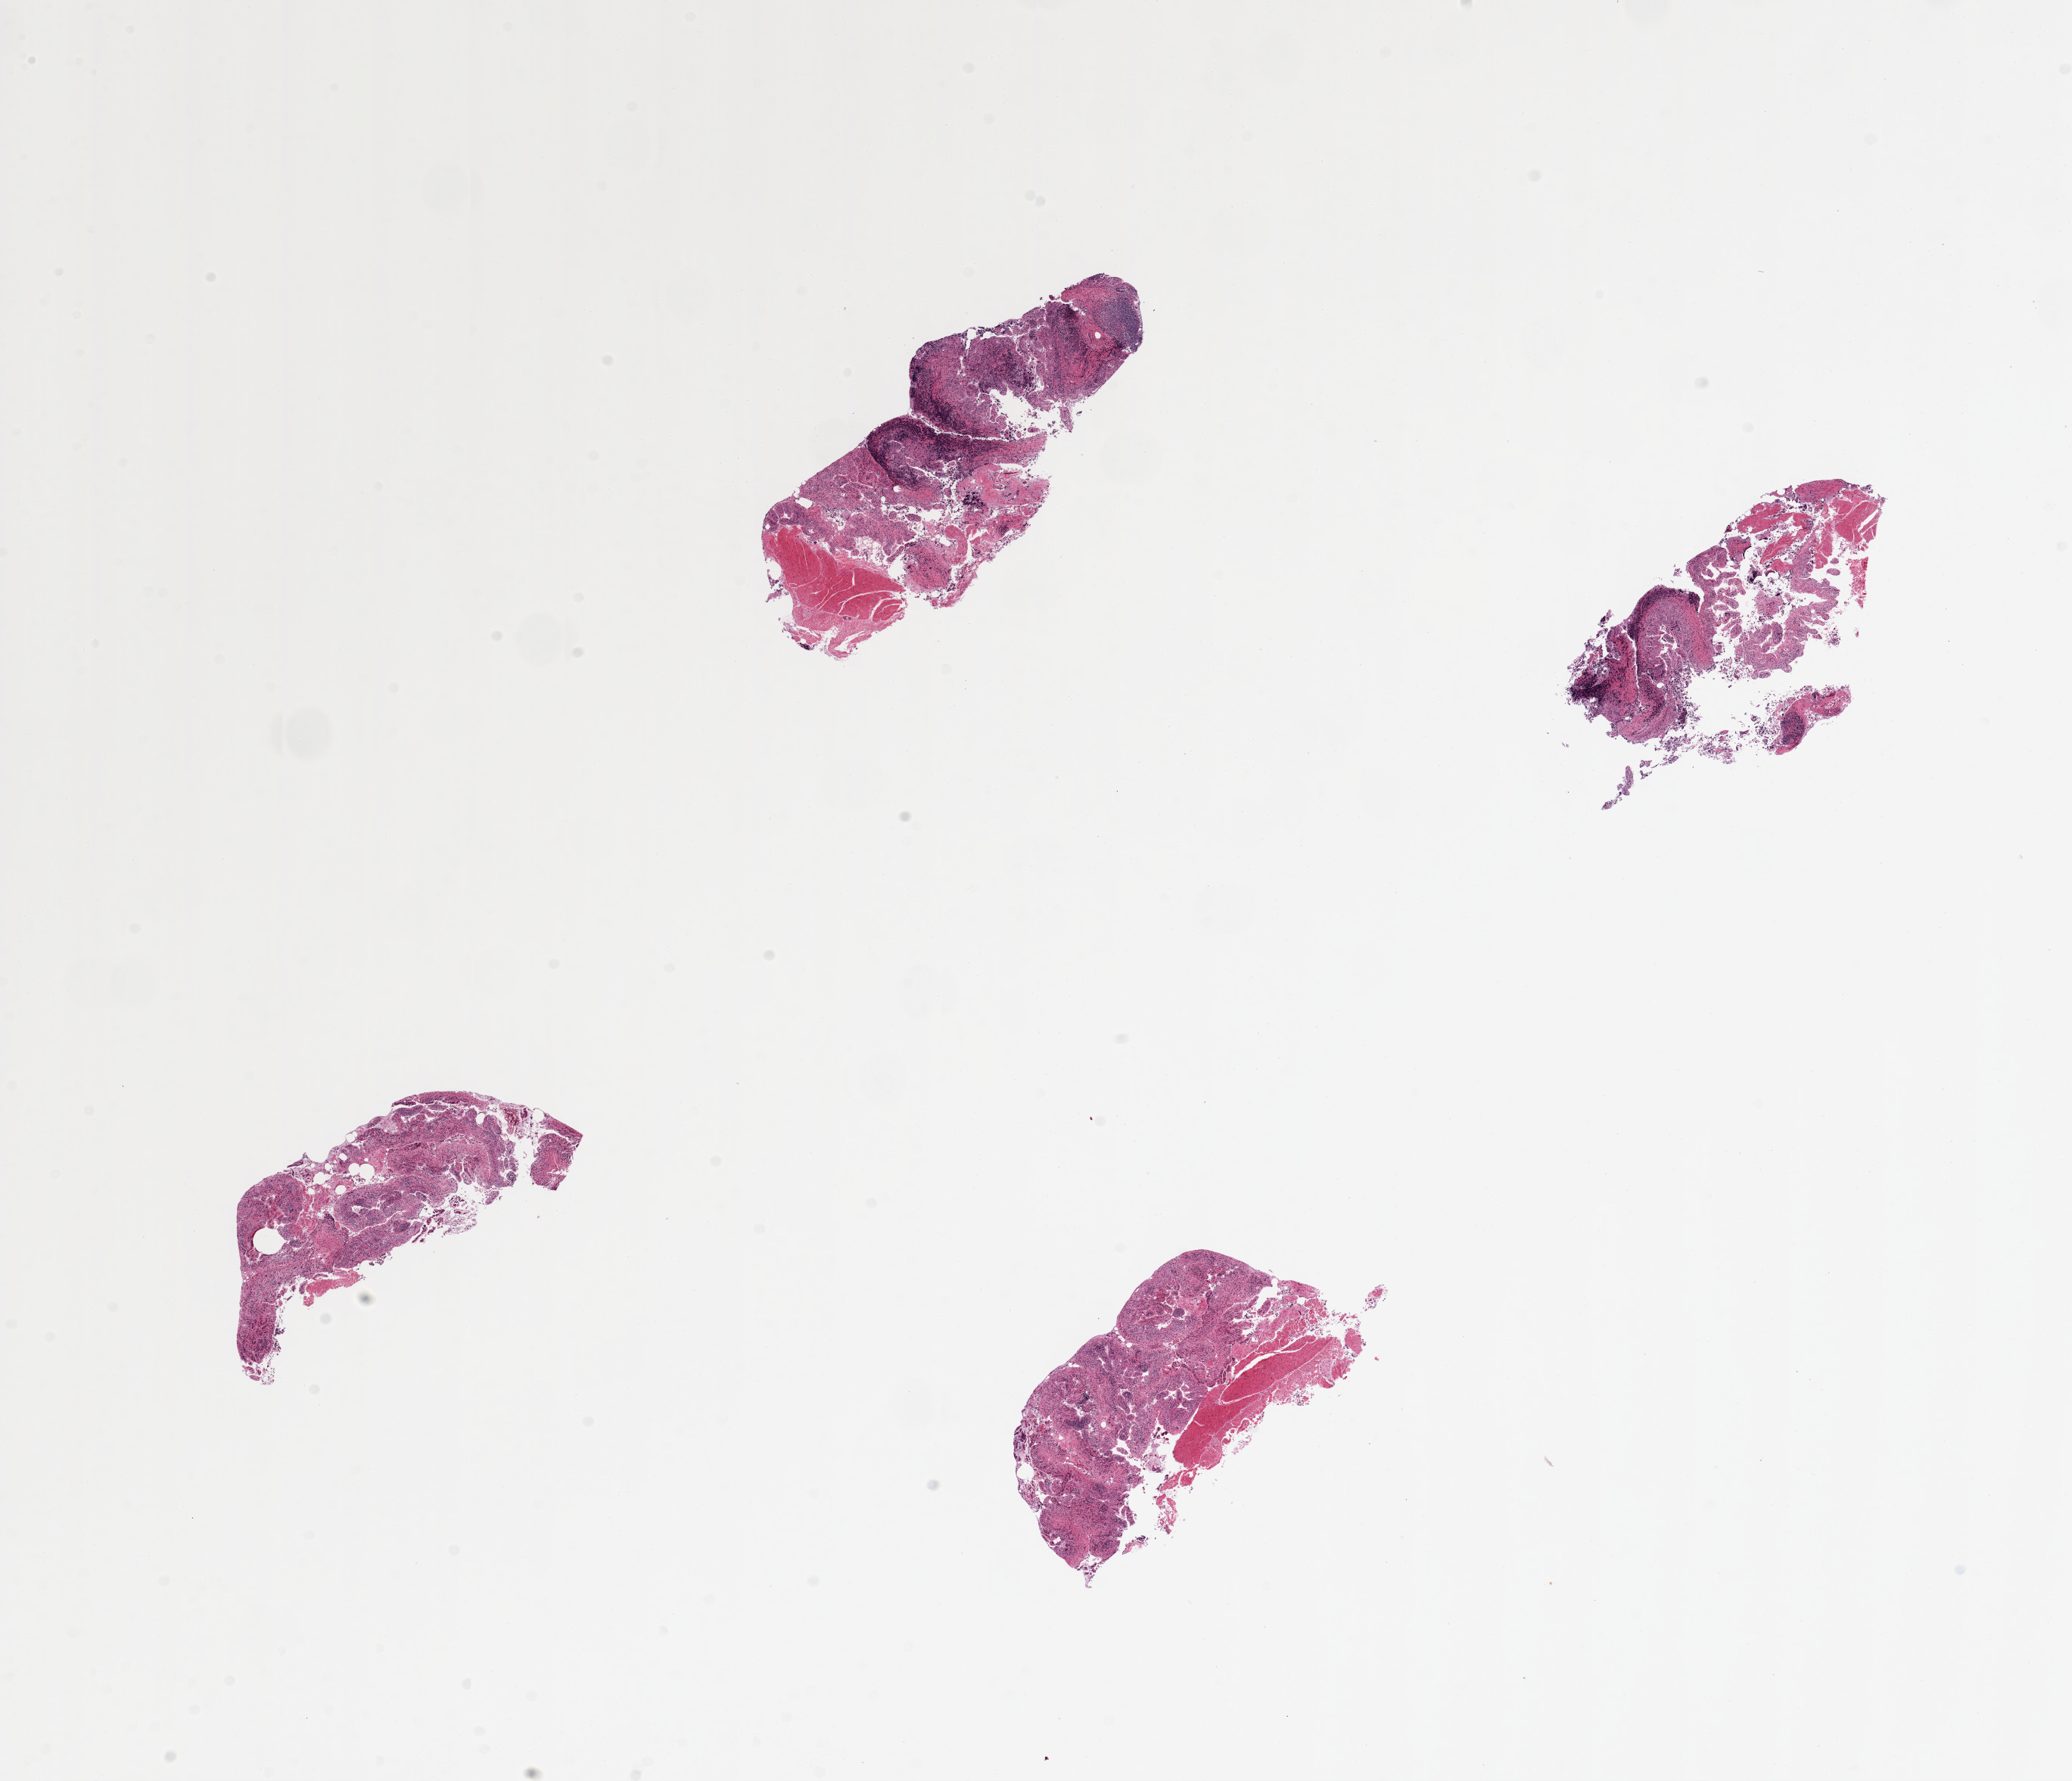
Hematoxylin and eosin (H&E) whole-slide image, brightfield — a low-resolution overview of the entire scanned area, about 21.7 x 18.6 mm, PAXgene-fixed, paraffin-embedded tissue, sampled site (target tissue): ileum, donor tissue sample. Donor: male.
Pathologist's review note for this sample: 4 pieces, ~30-40% lymphoid aggregates and lamina propria lymphoid cells; epithelial component totally autolyzed/sloughed.